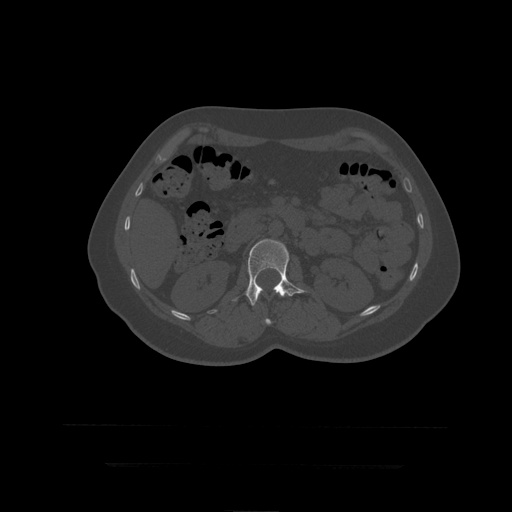
CT including the spine, one axial slice. Slice 153 of 399 in the series (ordered by position). Bone window (W 1800 / L 400 HU). 1.25 mm slice thickness. 512 × 512 image matrix, field of view 450 × 450 mm. Patient age 41 years. Case-level facts recorded for this patient, not image findings: primary cancer: breast.
Structures marked on this image (semi-automatic segmentation, software-assisted and operator-edited):
- L1 vertebra: box from (x=265, y=319) to (x=272, y=325) px
- L2 vertebra: (x=232, y=239)–(x=307, y=306)